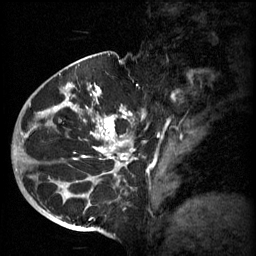
Breast MRI (dynamic contrast-enhanced), one sagittal slice; slice 37 of 60 in the series (ordered by position); 3 images stored at this slice position (order not interpretable as contrast timing); 1.5 T; TE 4.2 ms, TR 11 ms; 2 mm slice thickness; 256 × 256 image matrix. Female patient, age 51 years.
Structures marked on this image (semi-automatic segmentation, software-assisted and operator-edited):
- analysis volume of interest (the breast-tissue region the enhancement analysis was run in; not a lesion): bounding box [x1, y1, x2, y2] px = [48, 82, 161, 197]
- tumour enhancement mask (voxels above the 70 % enhancement threshold inside the analysis volume of interest): [48, 84, 138, 197]